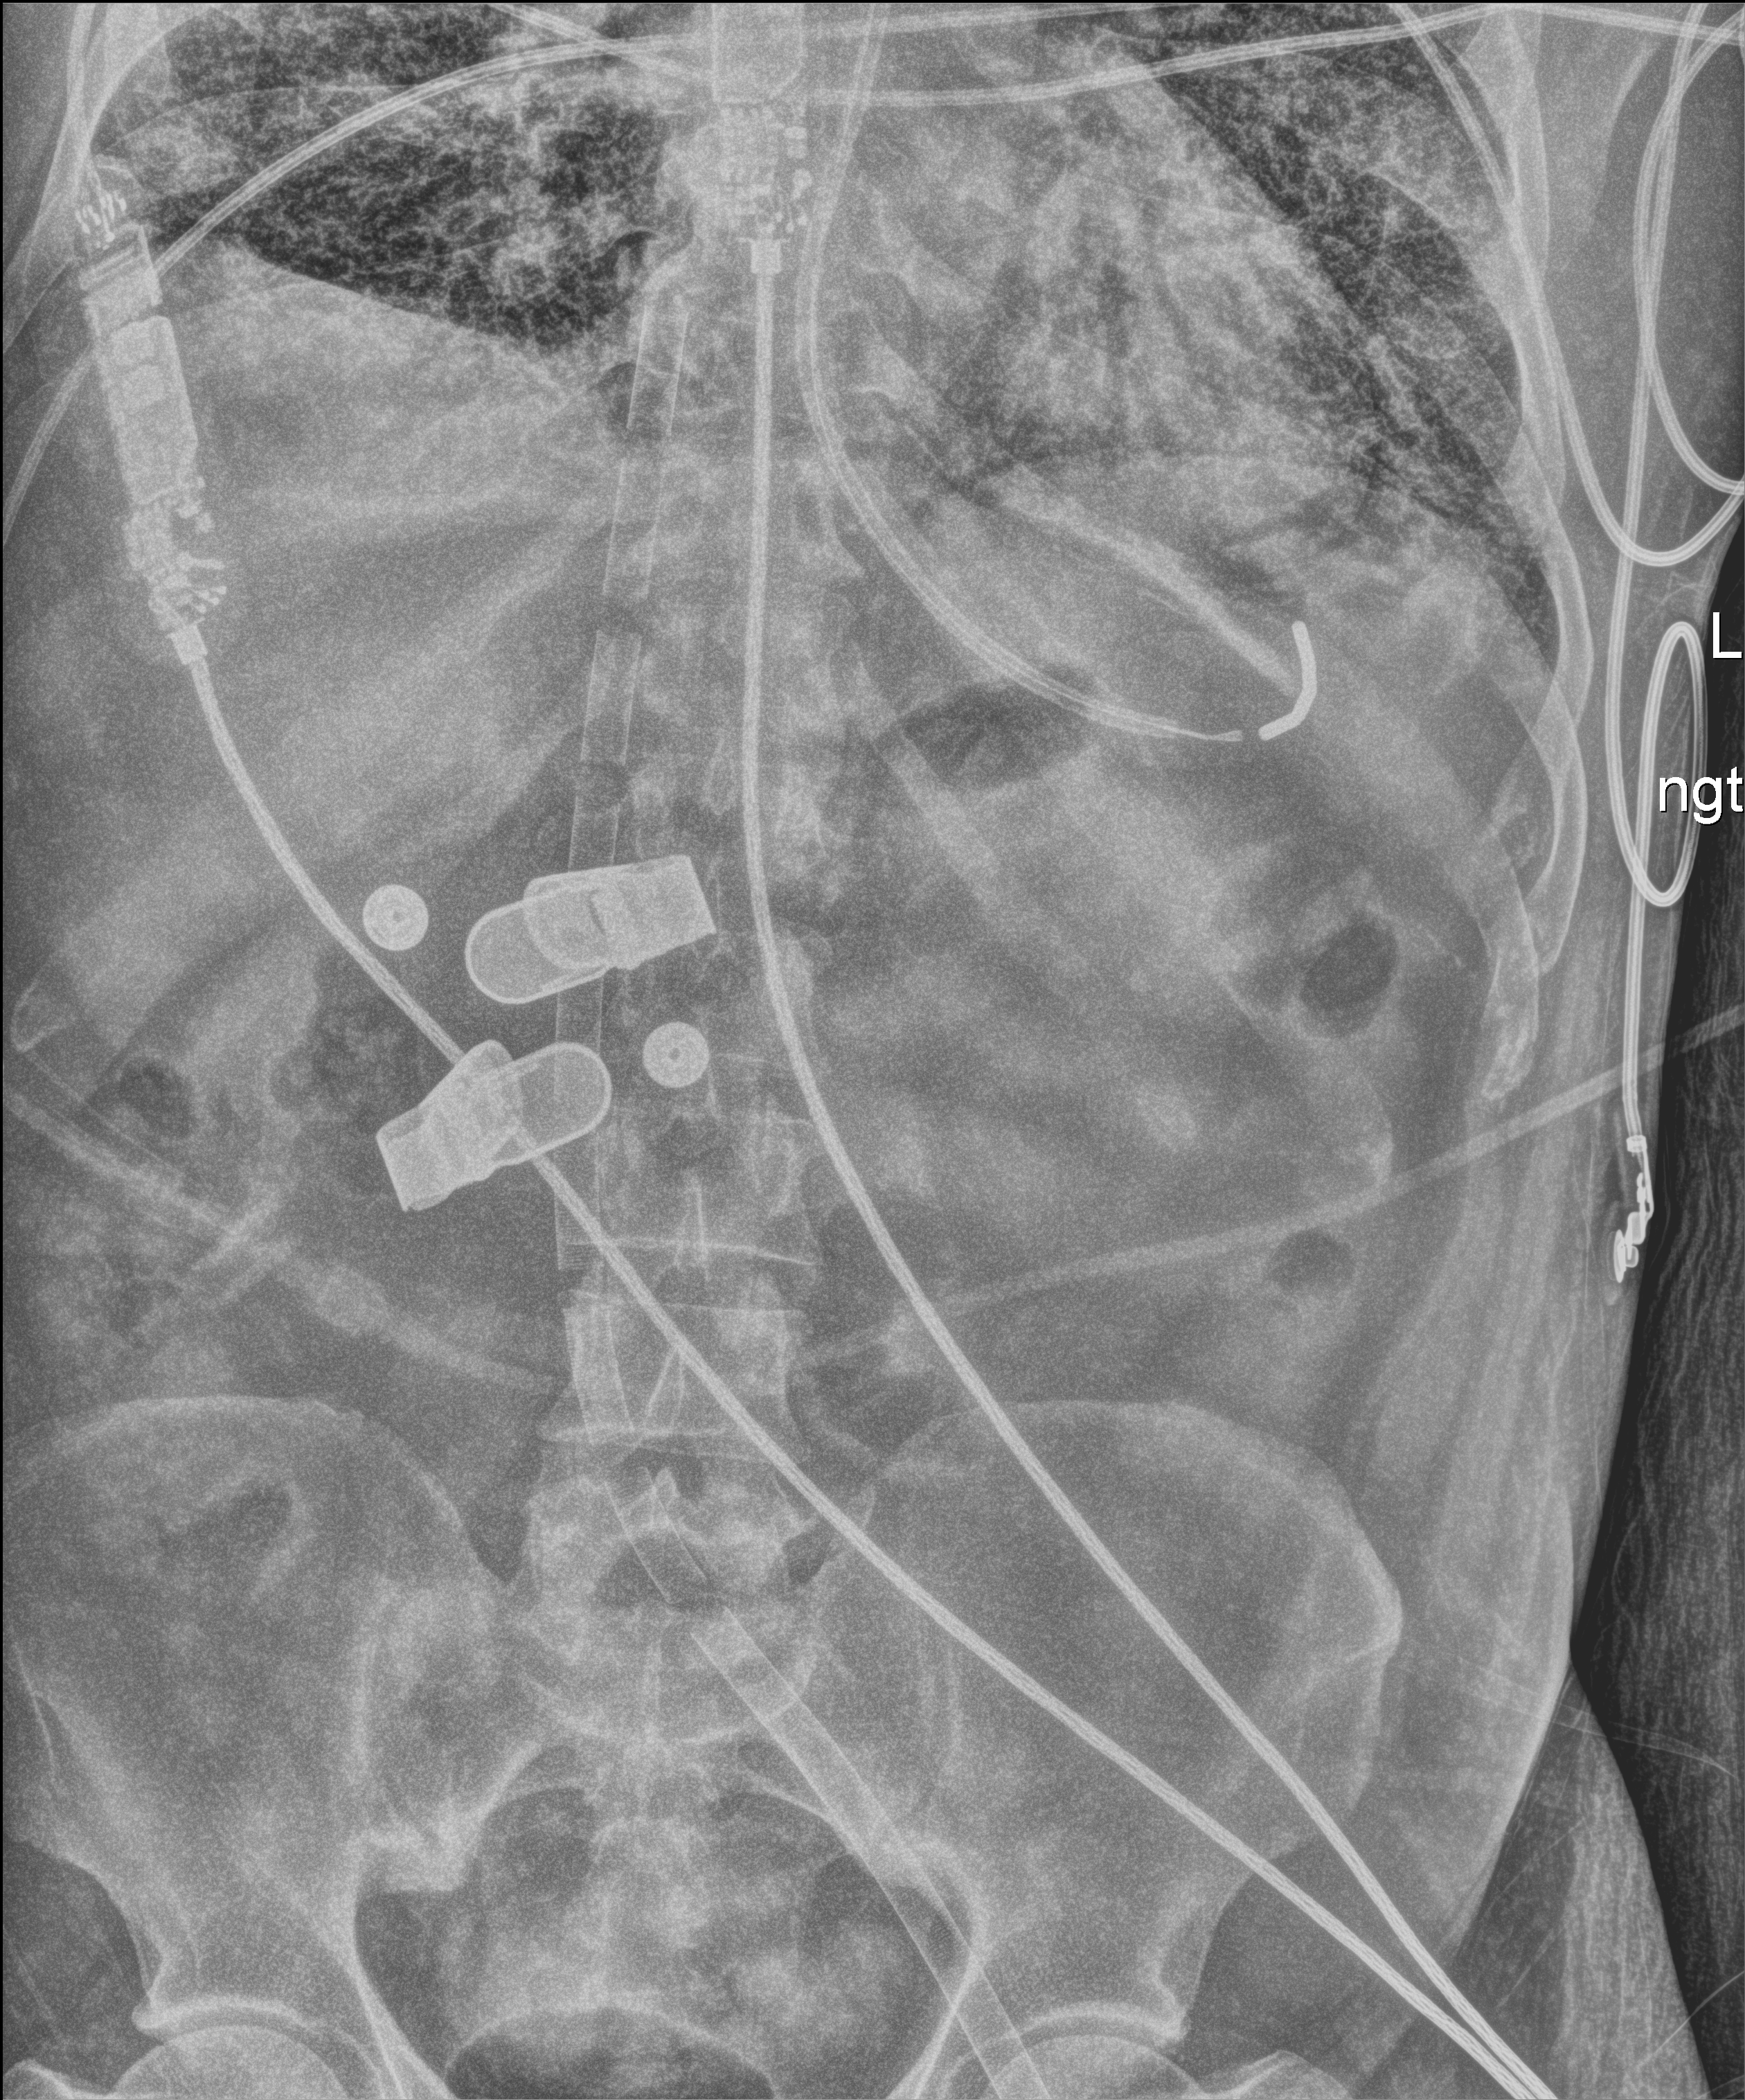
Bedside chest radiograph (digital radiography). Male patient hospitalised with COVID-19, age 18–59 years.
Hospital-stay facts (about this admission, not read from this image; timing relative to this image not recorded): COPD (admission record): no; other chronic lung disease (admission record): no.